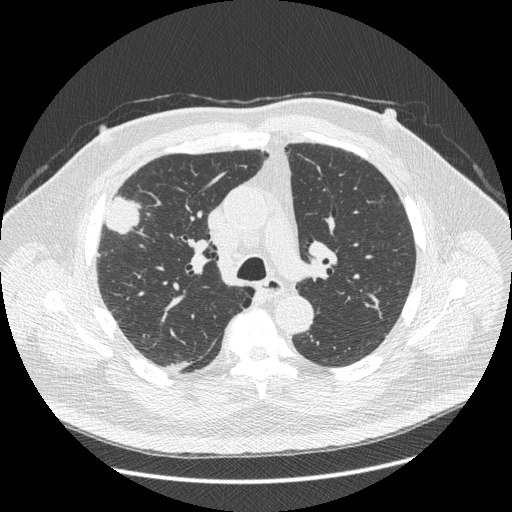
Axial slice from a low-dose chest CT screening exam; third annual screen; lung window (W 1500 / L -600 HU); 1.25 mm slice thickness; standard (soft-tissue) reconstruction kernel (STANDARD). Male participant, aged 66 years at enrolment. Current smoker at enrolment.
Expert-annotated lung lesion, bounding box [x1, y1, x2, y2] px = [86, 185, 145, 265]. Screening reader's record for this exam (one nodule recorded; not confirmed to be the boxed lesion): non-calcified nodule or mass ≥4 mm, right upper lobe, 48 × 25 mm, spiculated (stellate) margins, soft tissue attenuation, pre-existing on the prior screen: no. Official screen result: positive, other. Later outcome: lung cancer diagnosed 35 days after this screen — non-small cell carcinoma, right upper lobe, stage IV (AJCC 6th edition), 50 mm at pathology.